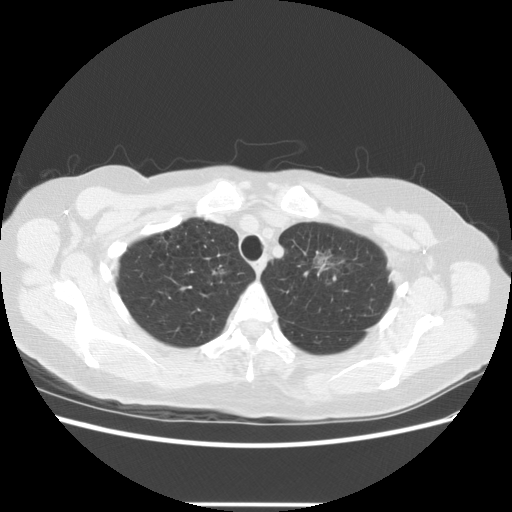
Low-dose screening chest CT, one axial slice. Slice 104 of 126 in the series (ordered by position). Lung window (W 1500 / L -600 HU). 512 × 512 image matrix.
Structures marked on this image (manually delineated by an expert):
- lesion 1 (tumor, upper lobe of right lung): bounding box <212,267,334,279> (left, top, right, bottom; pixels)
- lesion 2 (tumor, upper lobe of left lung): <313,255,330,272>